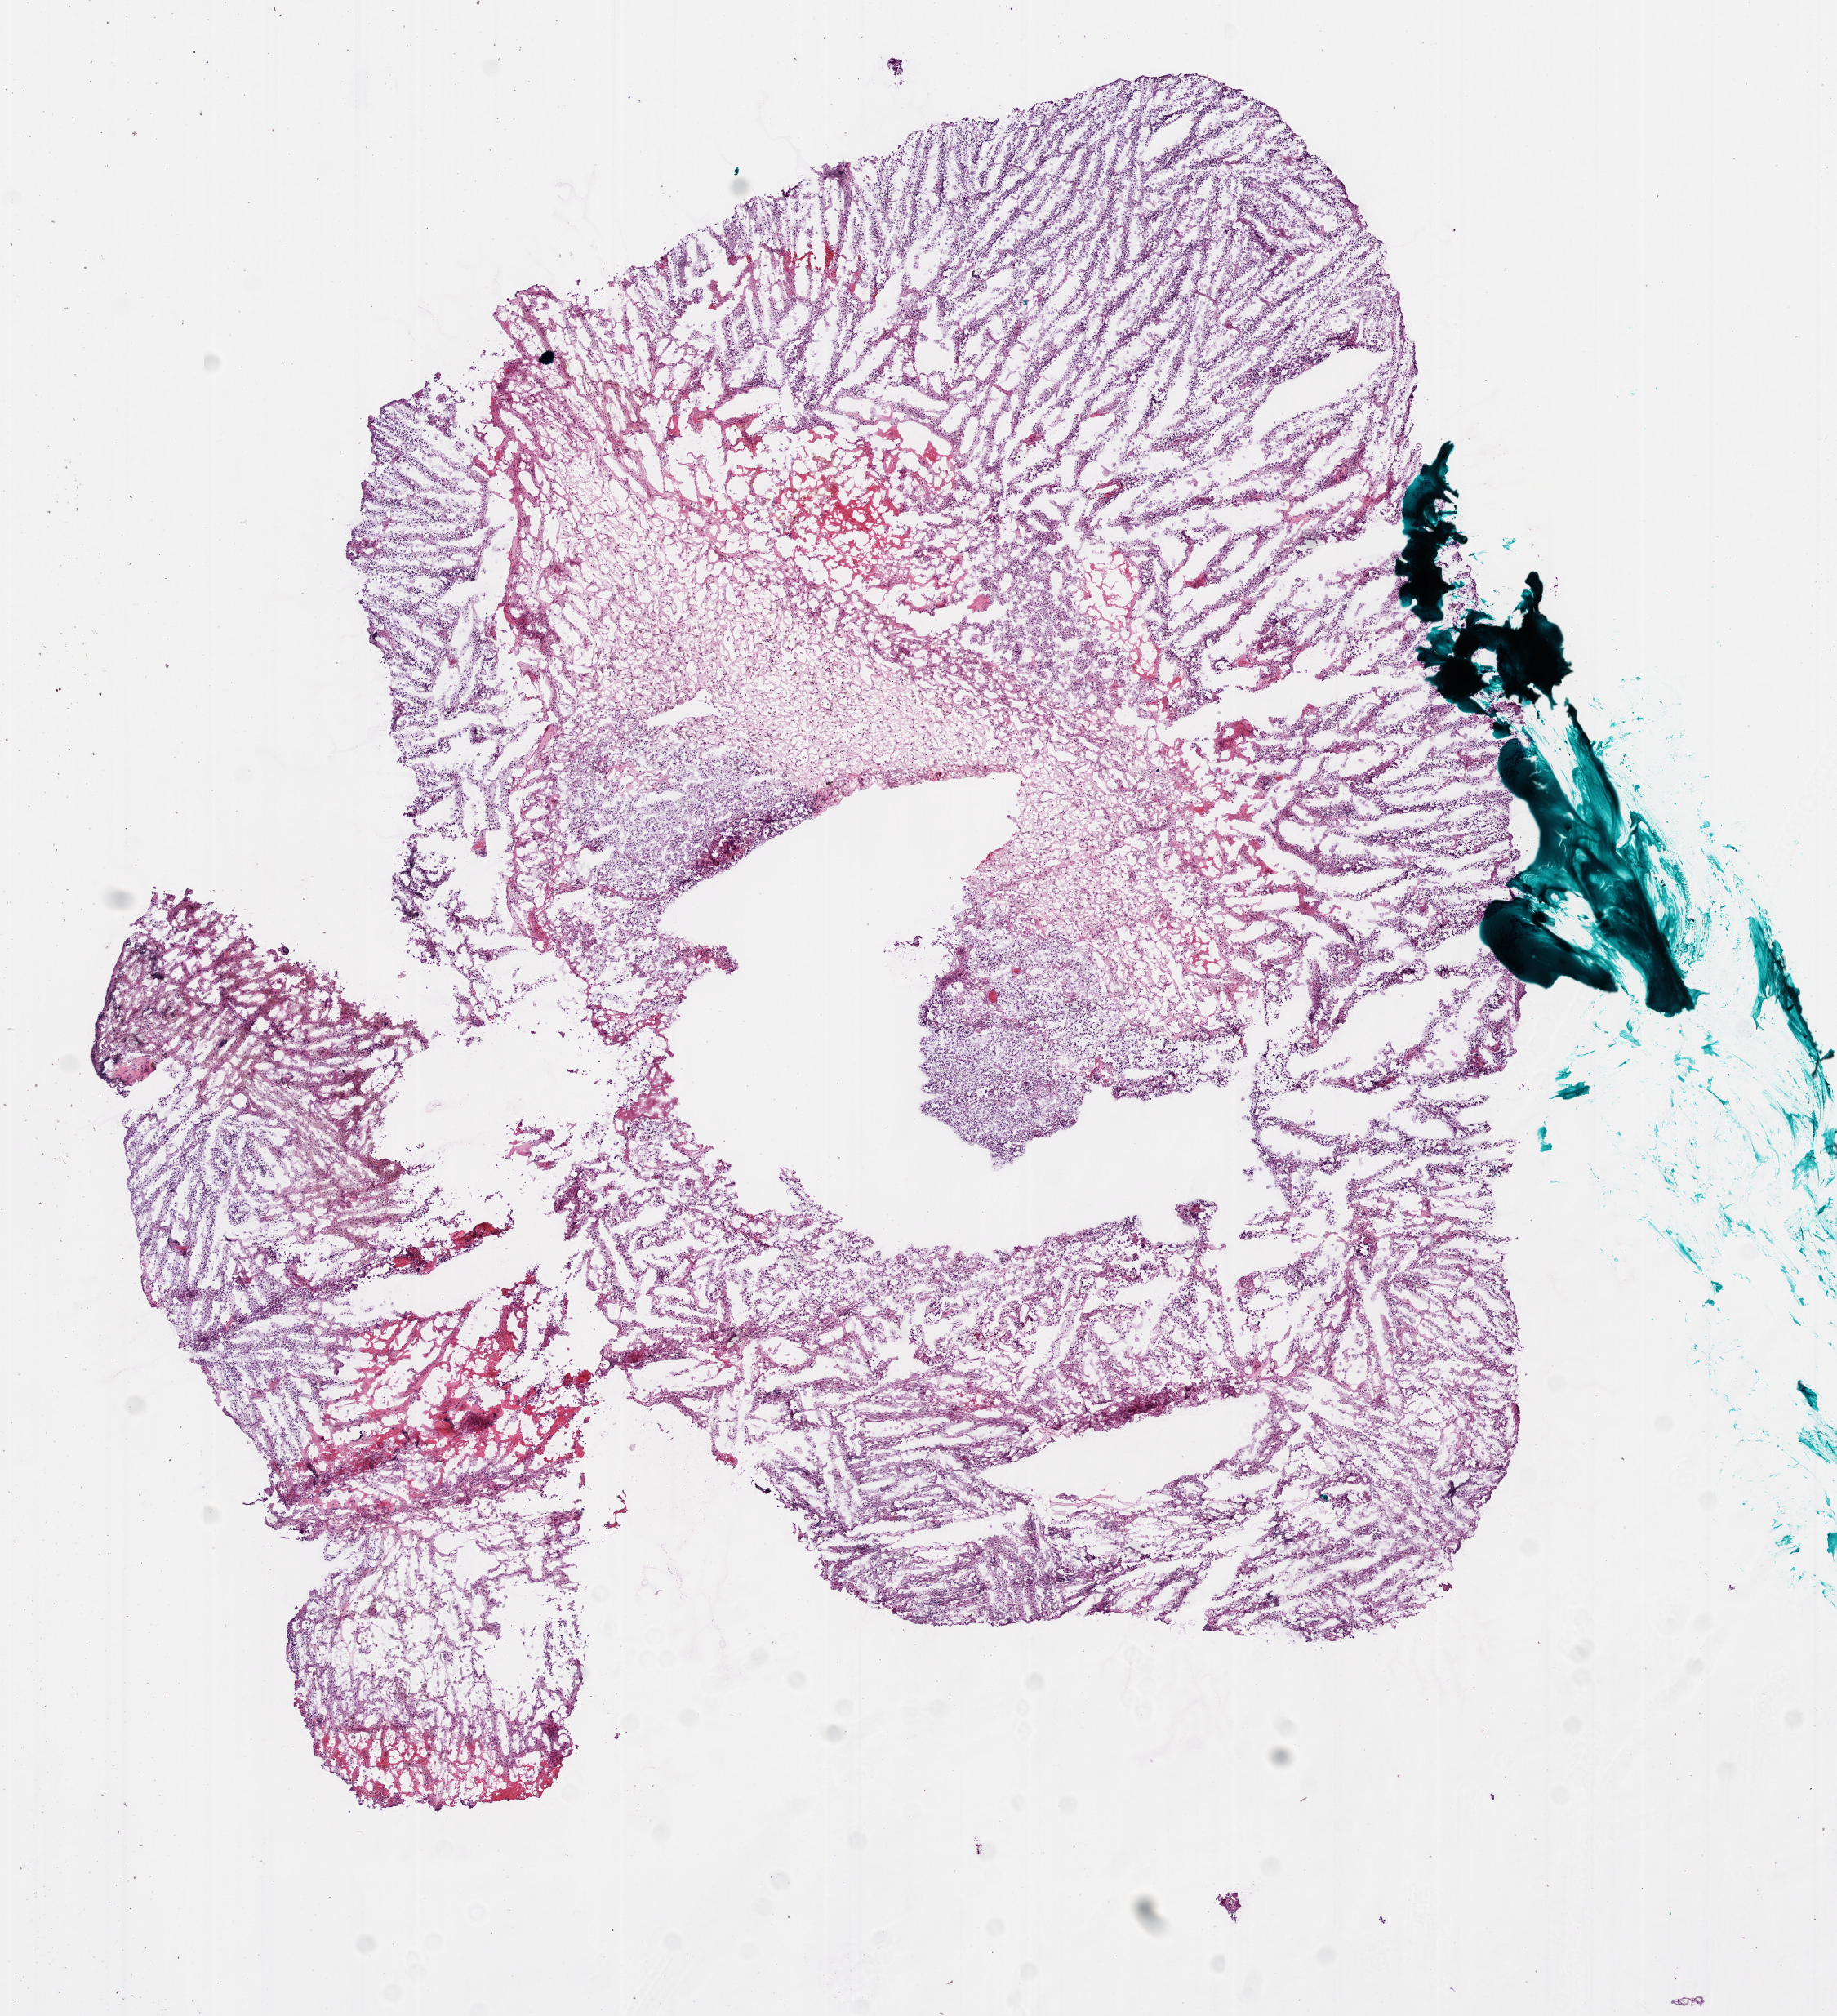
Whole-slide histology image, Hematoxylin and eosin (H&E) stained, whole scanned area (about 9.0 x 9.9 mm, slide scanned at 20x) shown as a low-resolution overview, frozen section from the bottom of the tissue portion, primary tumour sample from the brain. Male, age 40 years at initial diagnosis. Slide review estimates, as recorded: tumour cells 85%, tumour nuclei 100%, normal cells 0%, stromal cells 0%, necrosis 15%.
- histologic diagnosis: Glioblastoma